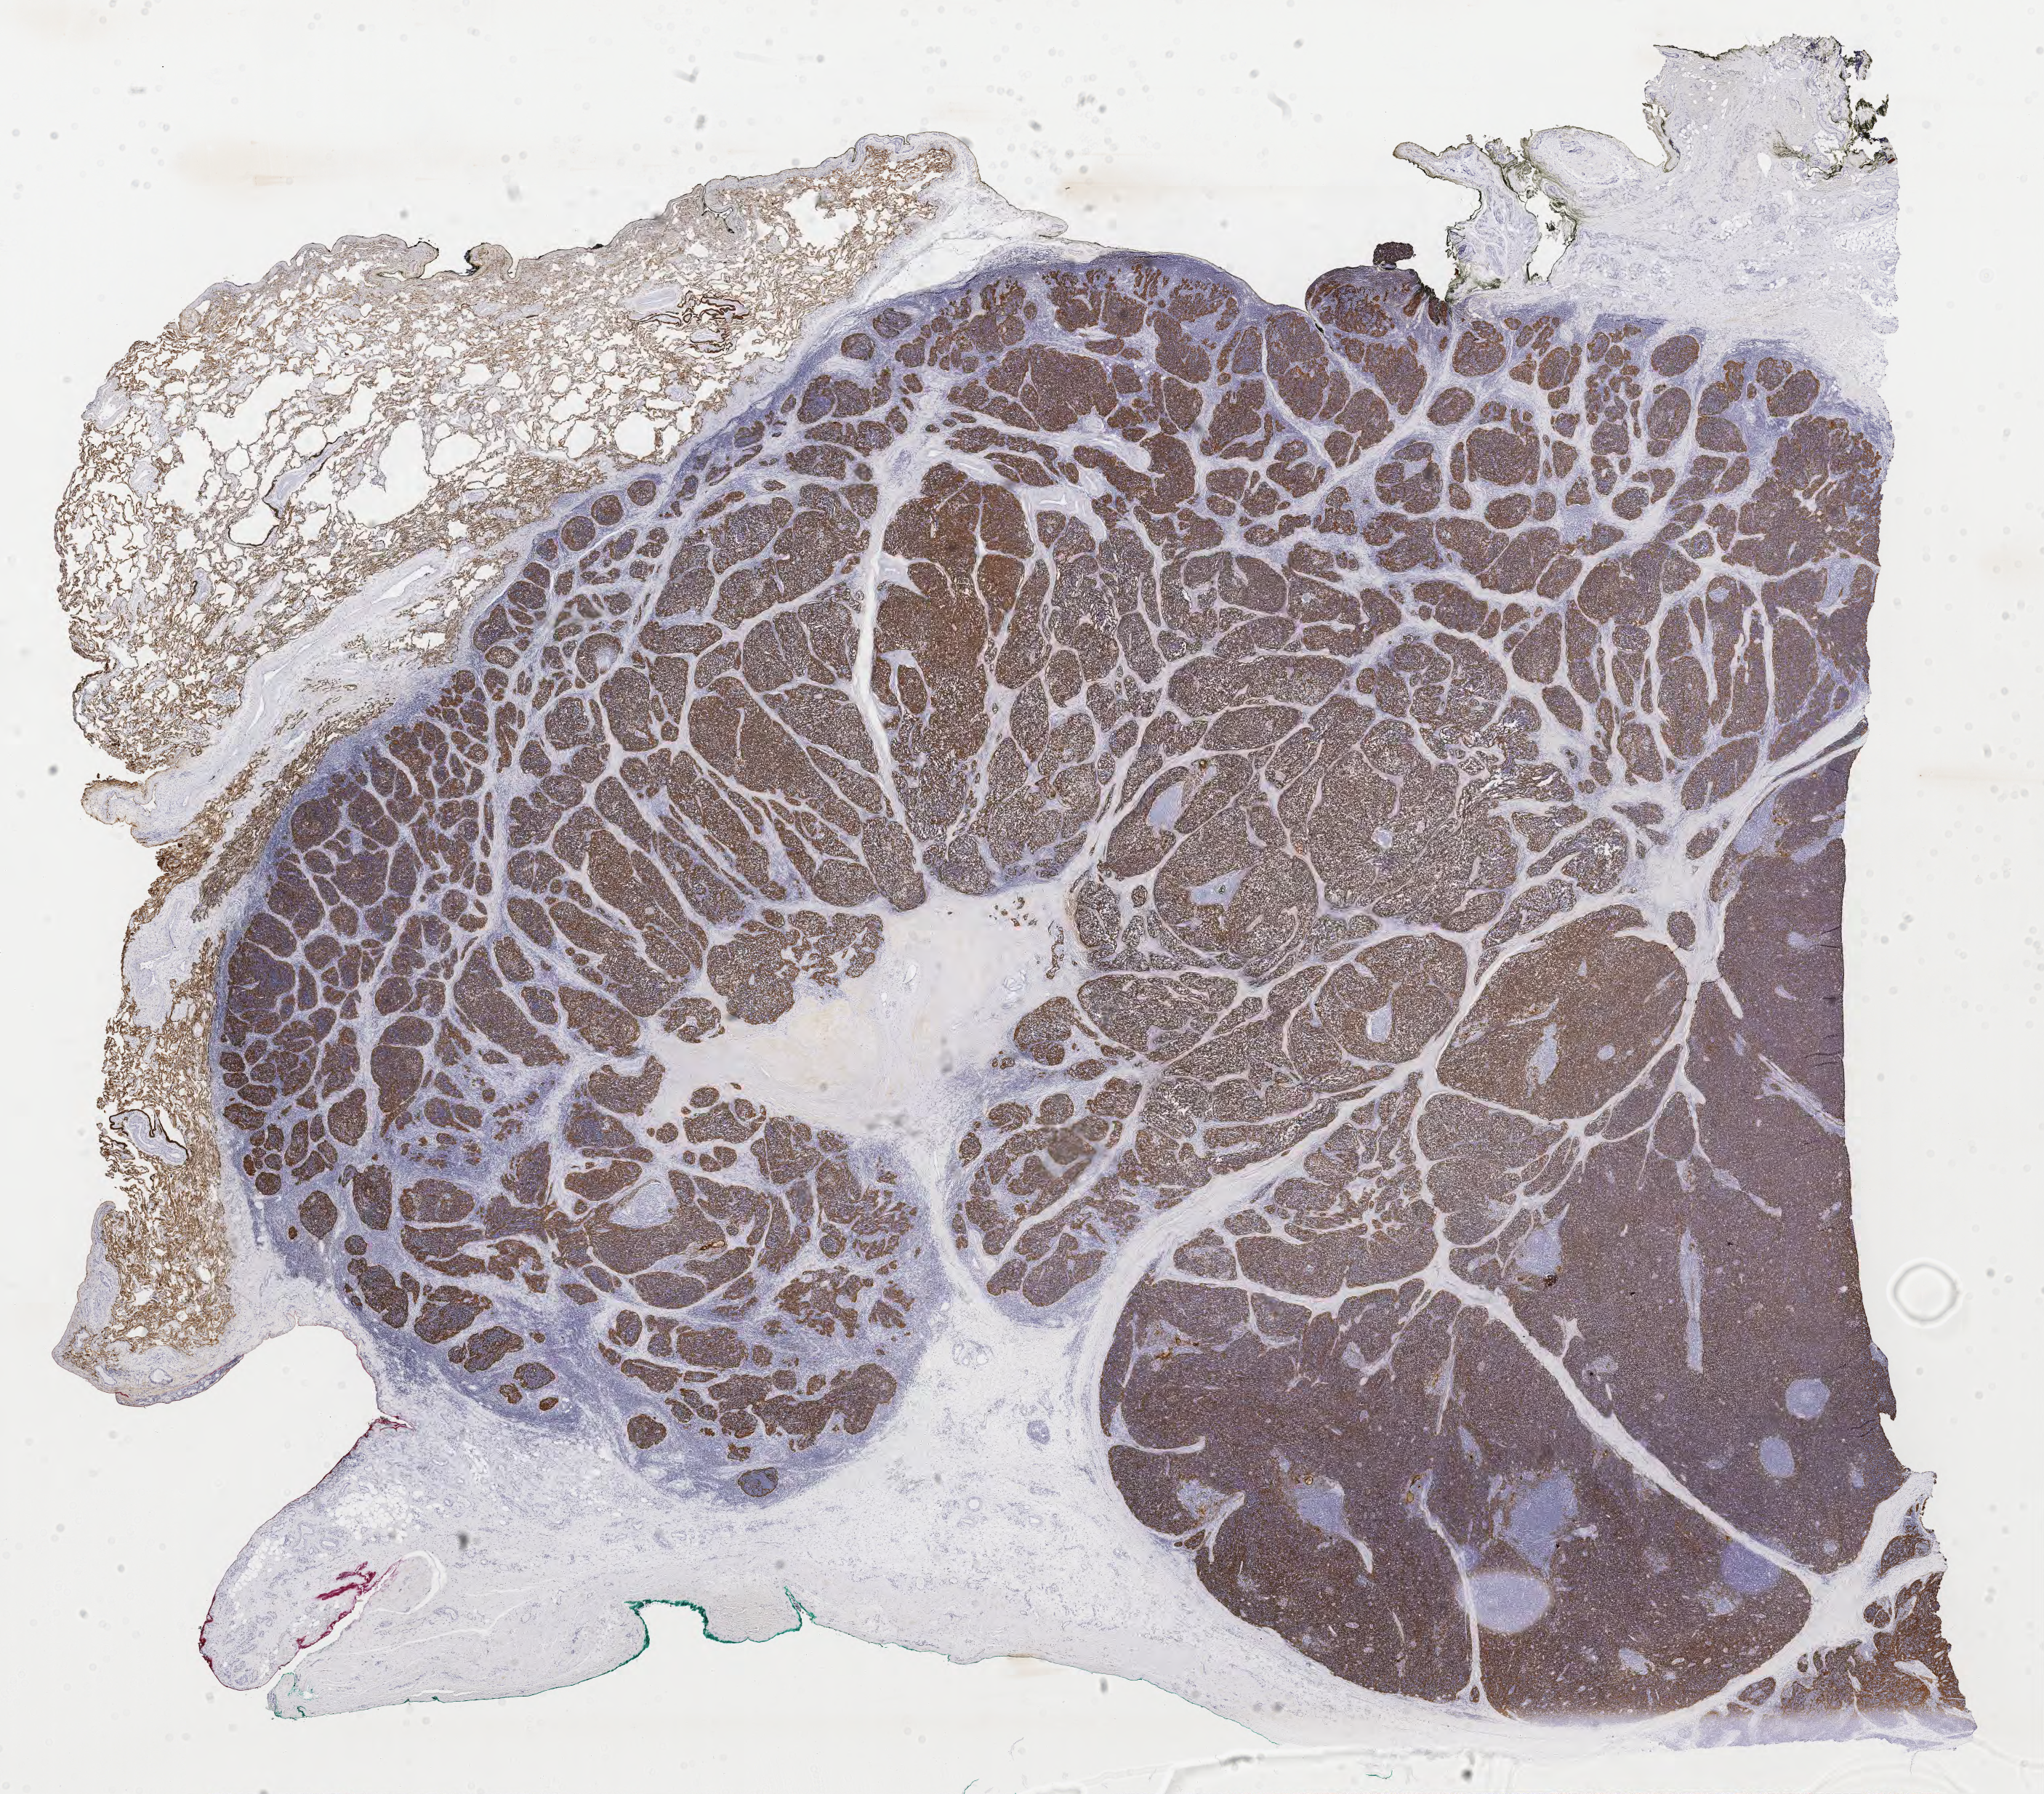
Whole-slide histology image, H&E-stained — a low-resolution overview of the entire scanned area, about 22.3 x 19.6 mm (slide scanned at 40x); FFPE section; thymus, primary tumour sample. Female patient; age at initial diagnosis 57 years.
• pathologic diagnosis: Thymoma, type B1, NOS